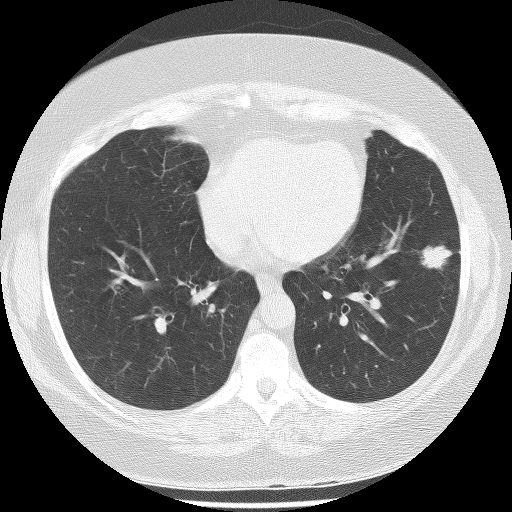
Low-dose screening chest CT, one axial slice. Position 103 of 233 along the scan axis. 120 kVp. Lung window (W 1500 / L -600 HU). 2.5 mm slice thickness. 512 × 512 image matrix, field of view 340 × 340 mm.
Outlined on this slice (expert manual segmentation):
- lesion 1 (tumor, lower lobe of left lung): bounding box [x1, y1, x2, y2] px = [421, 245, 452, 269]